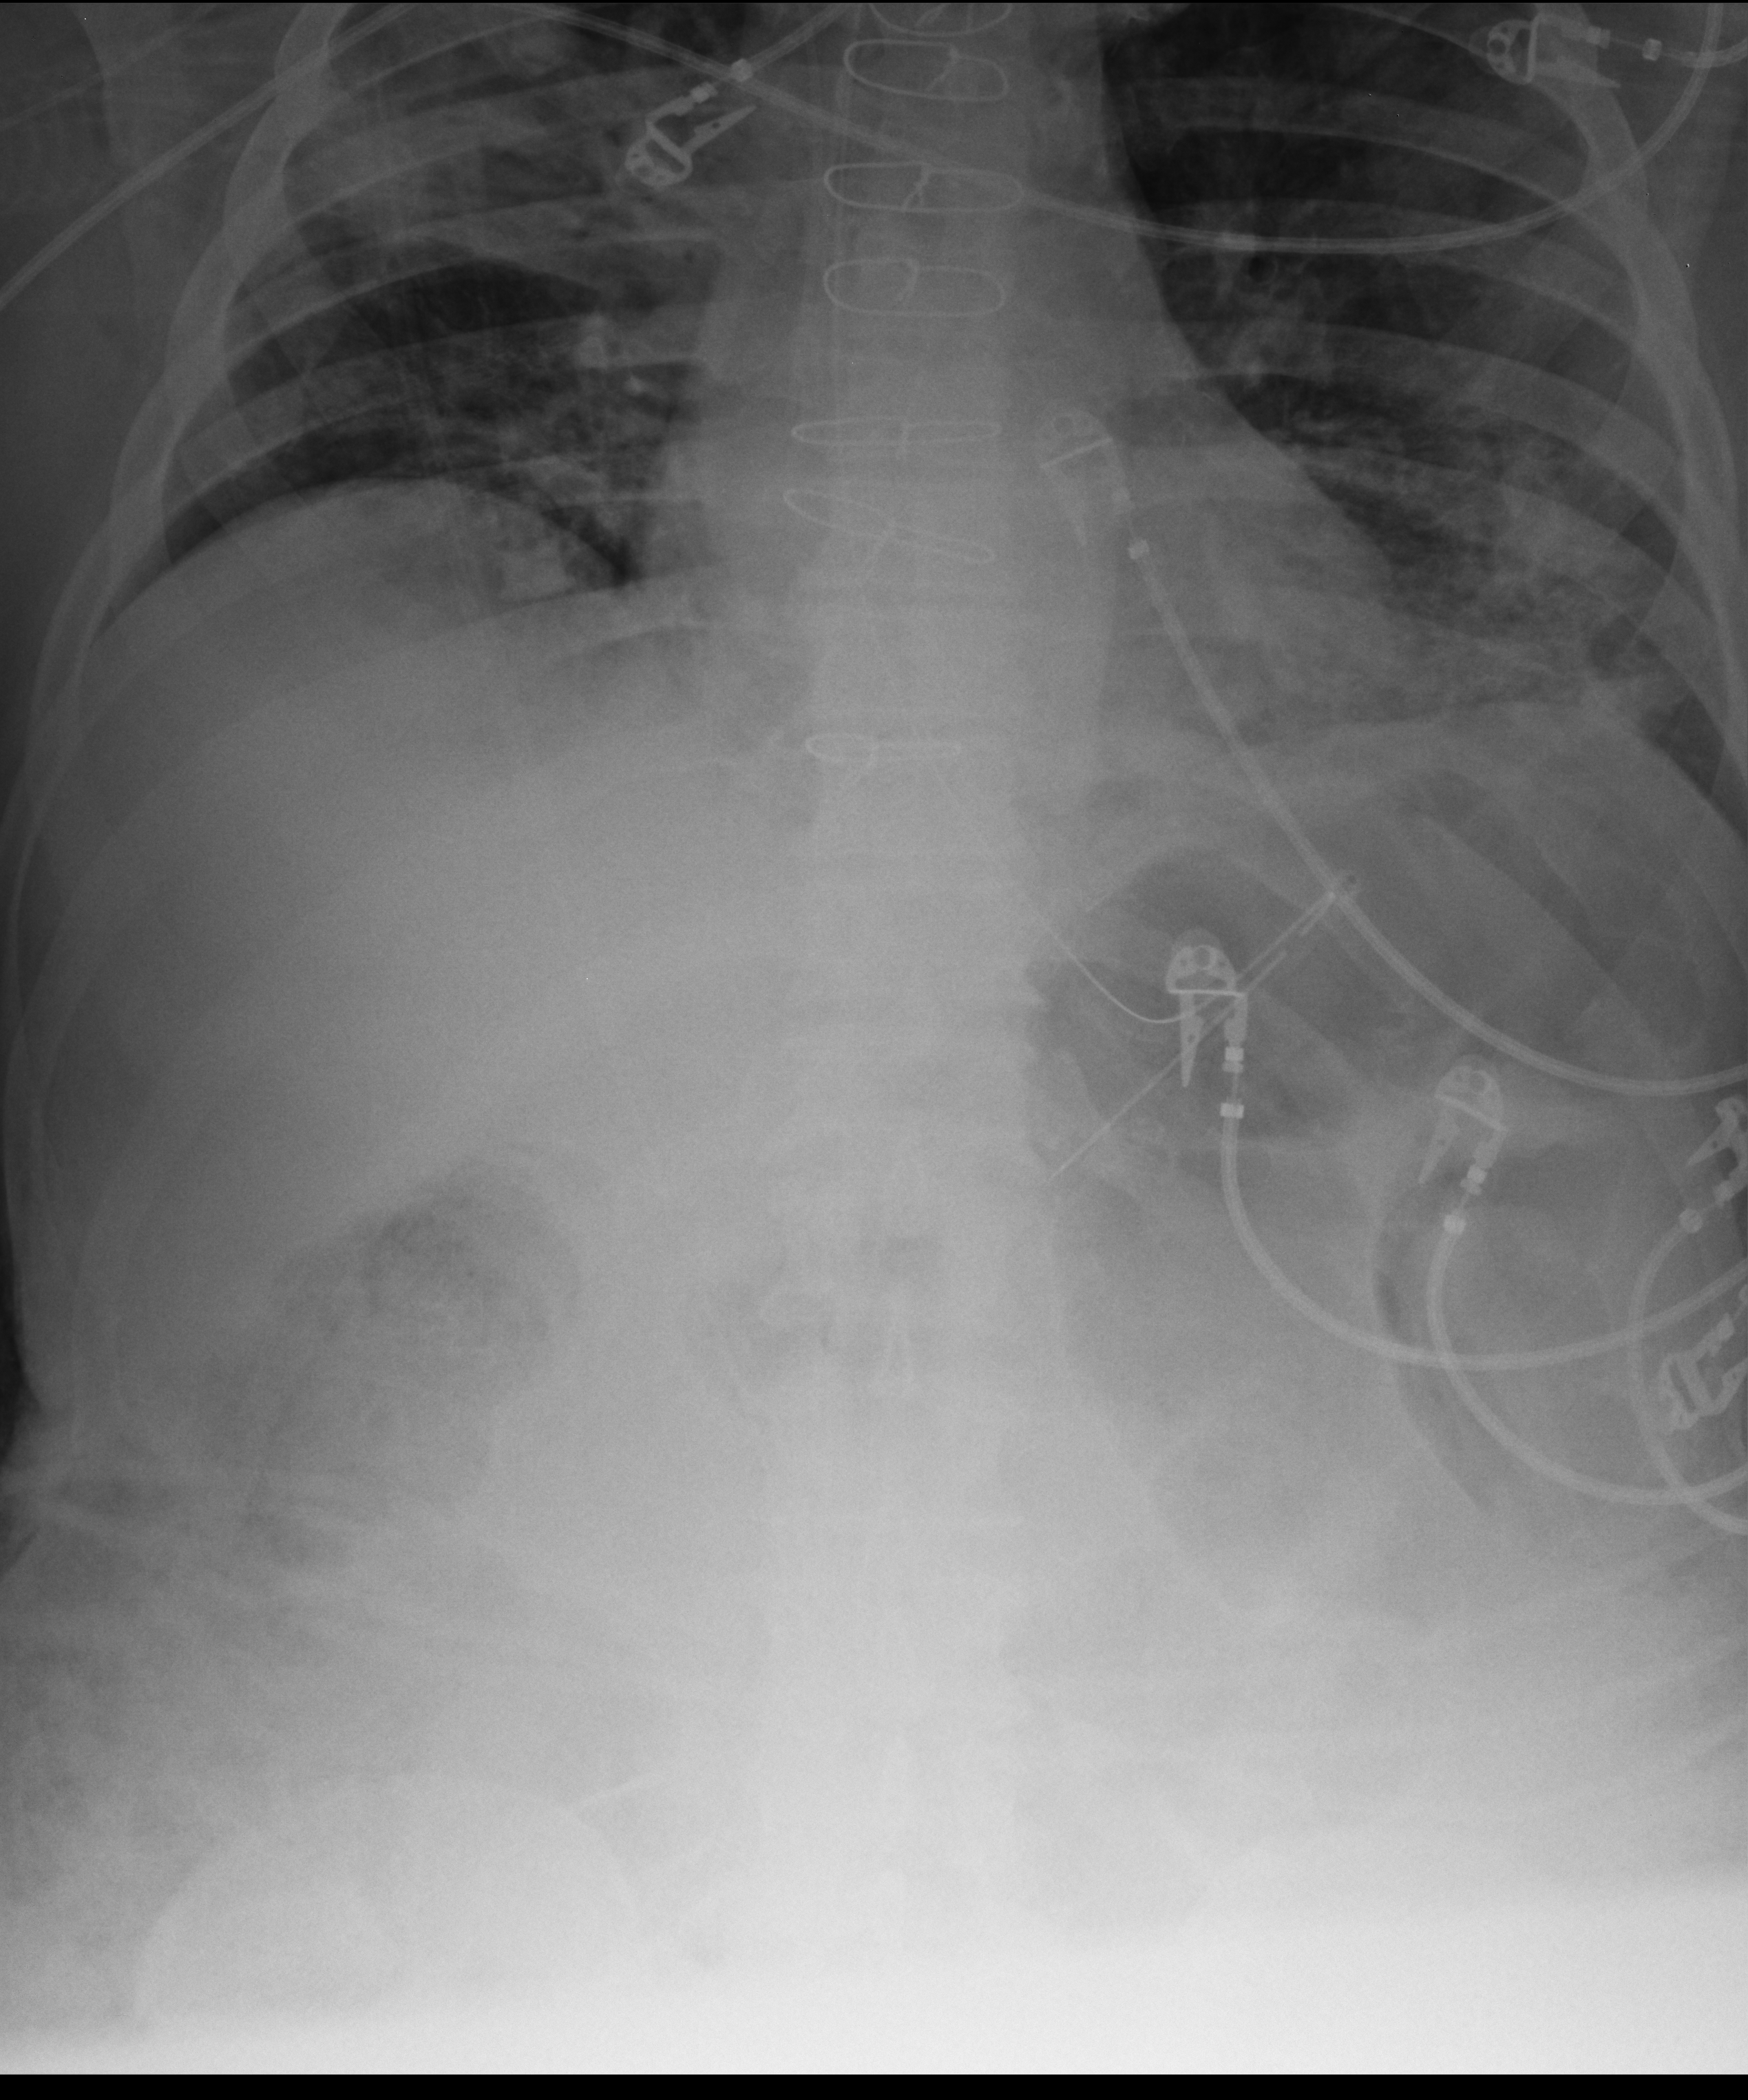
Bedside chest radiograph (computed radiography). Patient hospitalised with COVID-19; male, aged 60–74 years.
Admission-level facts for this patient (not findings on this image; timing relative to this image not recorded):
- mechanically ventilated during this hospital stay: yes
- chronic kidney disease (admission record): no
- smoking status (admission record): former